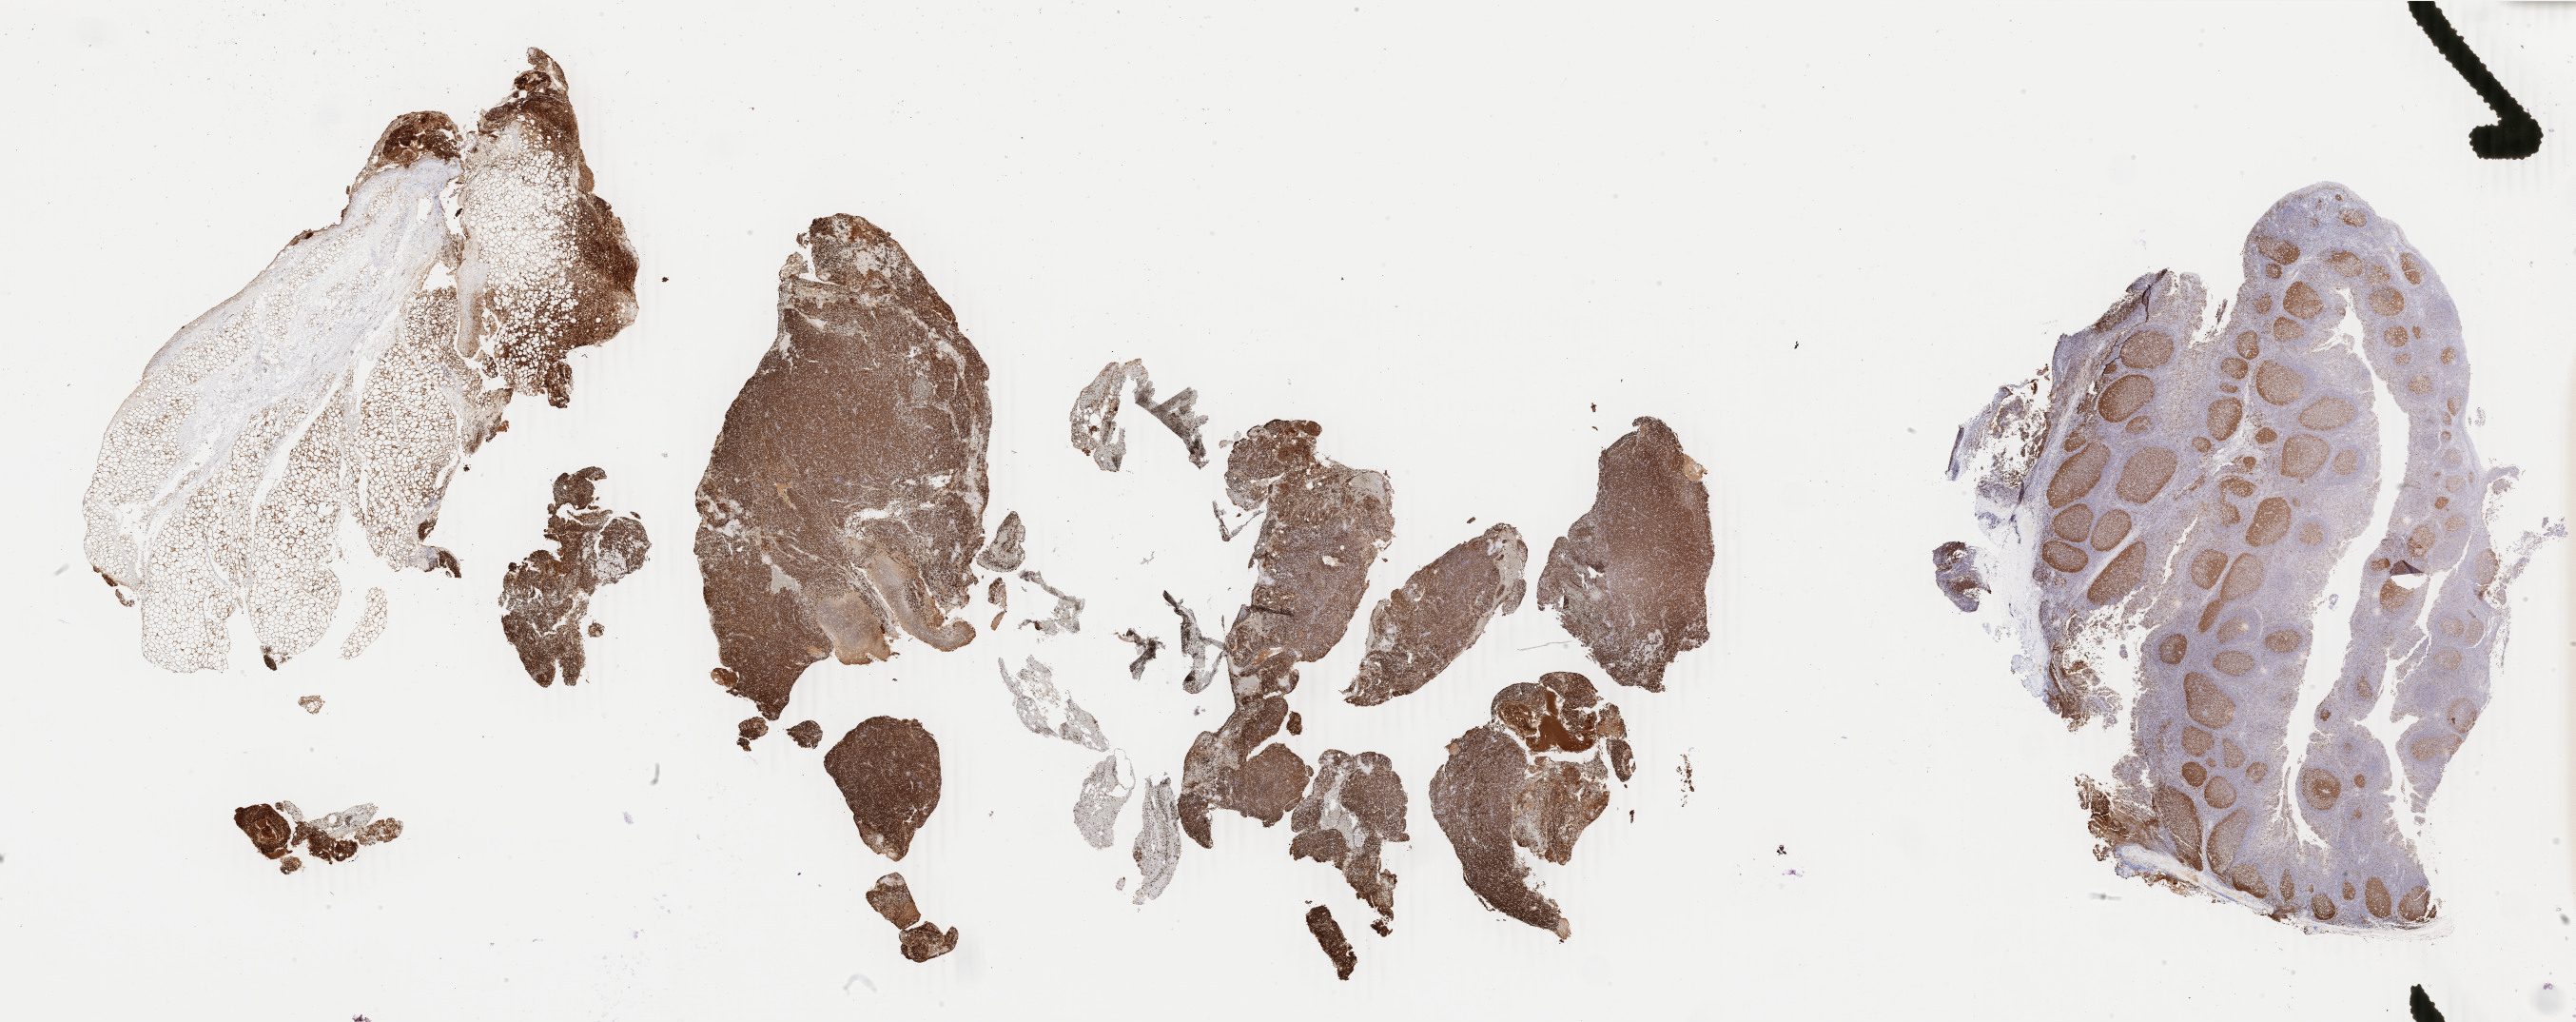
Immunohistochemistry (IHC) whole-slide image stained for Ki-67 — whole scanned area (about 43.1 x 17.1 mm) shown as a low-resolution overview, tumor tissue, site: abdominal lymph node. Male patient, 27 years old.
Diagnosis: Burkitt lymphoma, NOS.